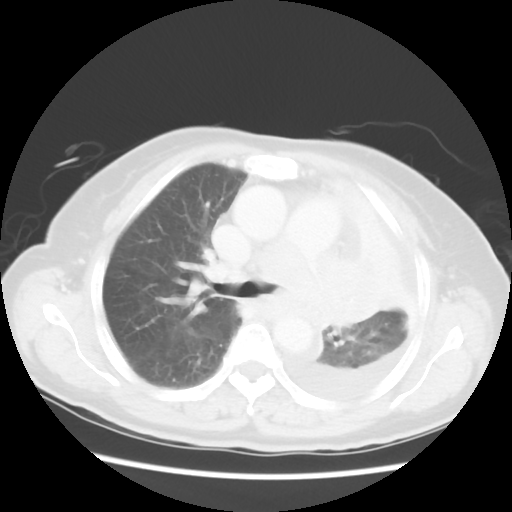
Chest CT, one axial slice; slice 35 of 52 in the series (ordered by position); 120 kVp; lung window (W 1500 / L -600 HU); 5 mm slice thickness; 512 × 512 image matrix. Female patient, age 72 years. From the clinical record (not read from this slice): clinical TNM (as recorded): T4 N3 M1b.
Structures marked on this image (bounding box drawn by a radiologist):
- lung tumour (recorded histology: large cell carcinoma): bounding box [x1, y1, x2, y2] px = [296, 245, 392, 339]